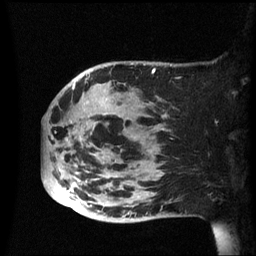
Breast MRI (dynamic contrast-enhanced), one sagittal slice. Slice 19 of 60 in the series (ordered by position). Dynamic contrast-enhanced series, image 2 of 3 at this slice position (ordered by acquisition). 1.5 T. TE 4.2 ms, TR 8.4 ms. 256 × 256 image matrix, field of view 230 × 230 mm. Patient: female, 49 years.
Outlined on this slice (semi-automatic segmentation, software-assisted and operator-edited):
- analysis volume of interest (the breast-tissue region the enhancement analysis was run in; not a lesion): bounding box (x1, y1, x2, y2) in pixels: (41, 61, 174, 223)
- tumour enhancement mask (voxels above the 70 % enhancement threshold inside the analysis volume of interest): (66, 70, 163, 219)